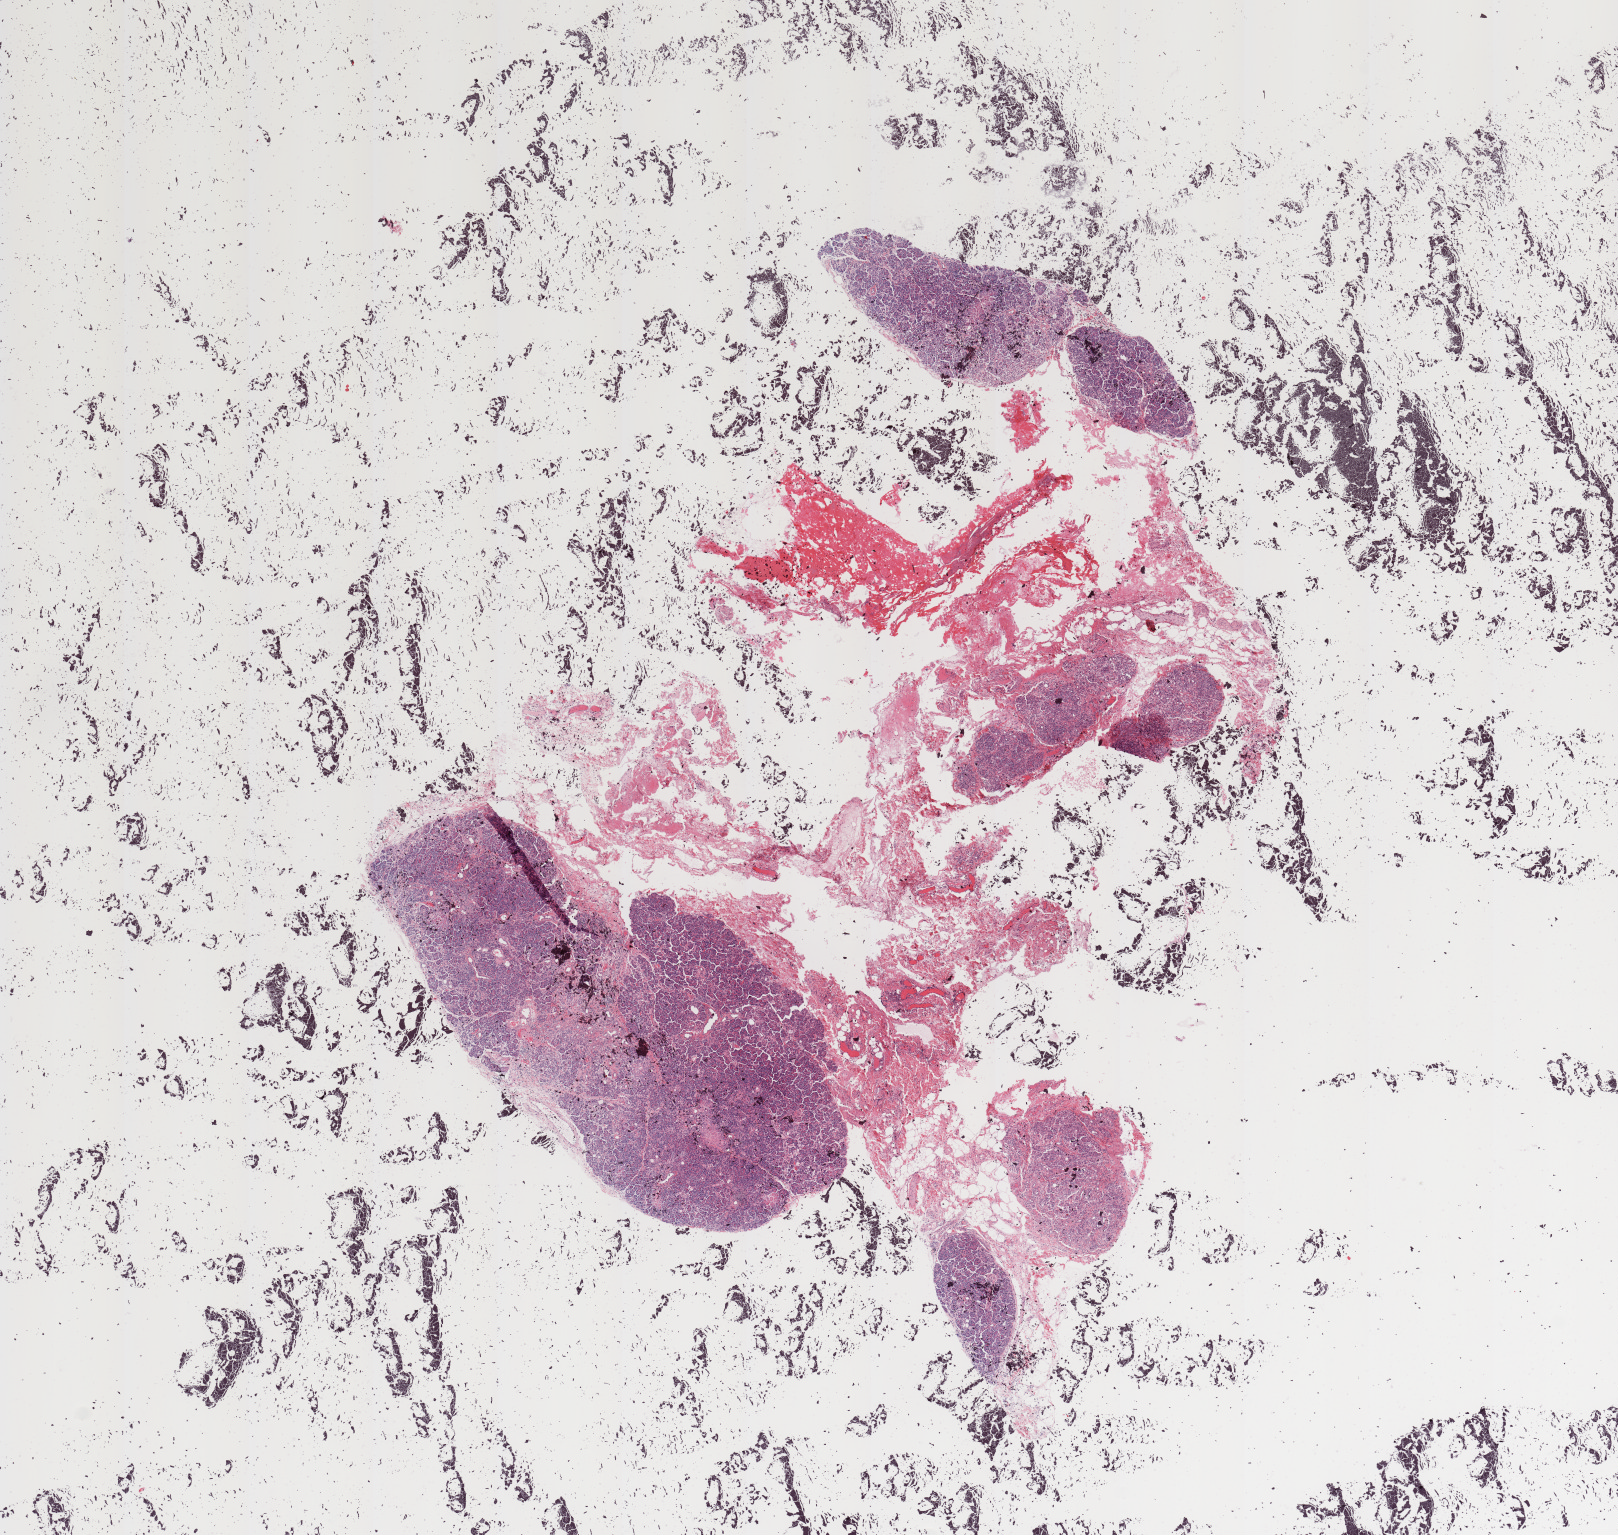
Whole-slide histology image, Hematoxylin and eosin (H&E) stained — low-resolution overview of the scanned area, about 12.8 x 12.1 mm (slide scanned at 20x), normal (non-tumour) tissue sample, pancreas. 67-year-old female patient.
This section: normal (non-tumour) tissue from the same patient. Patient diagnosis (cohort enrolment): ductal adenocarcinoma (pancreas).